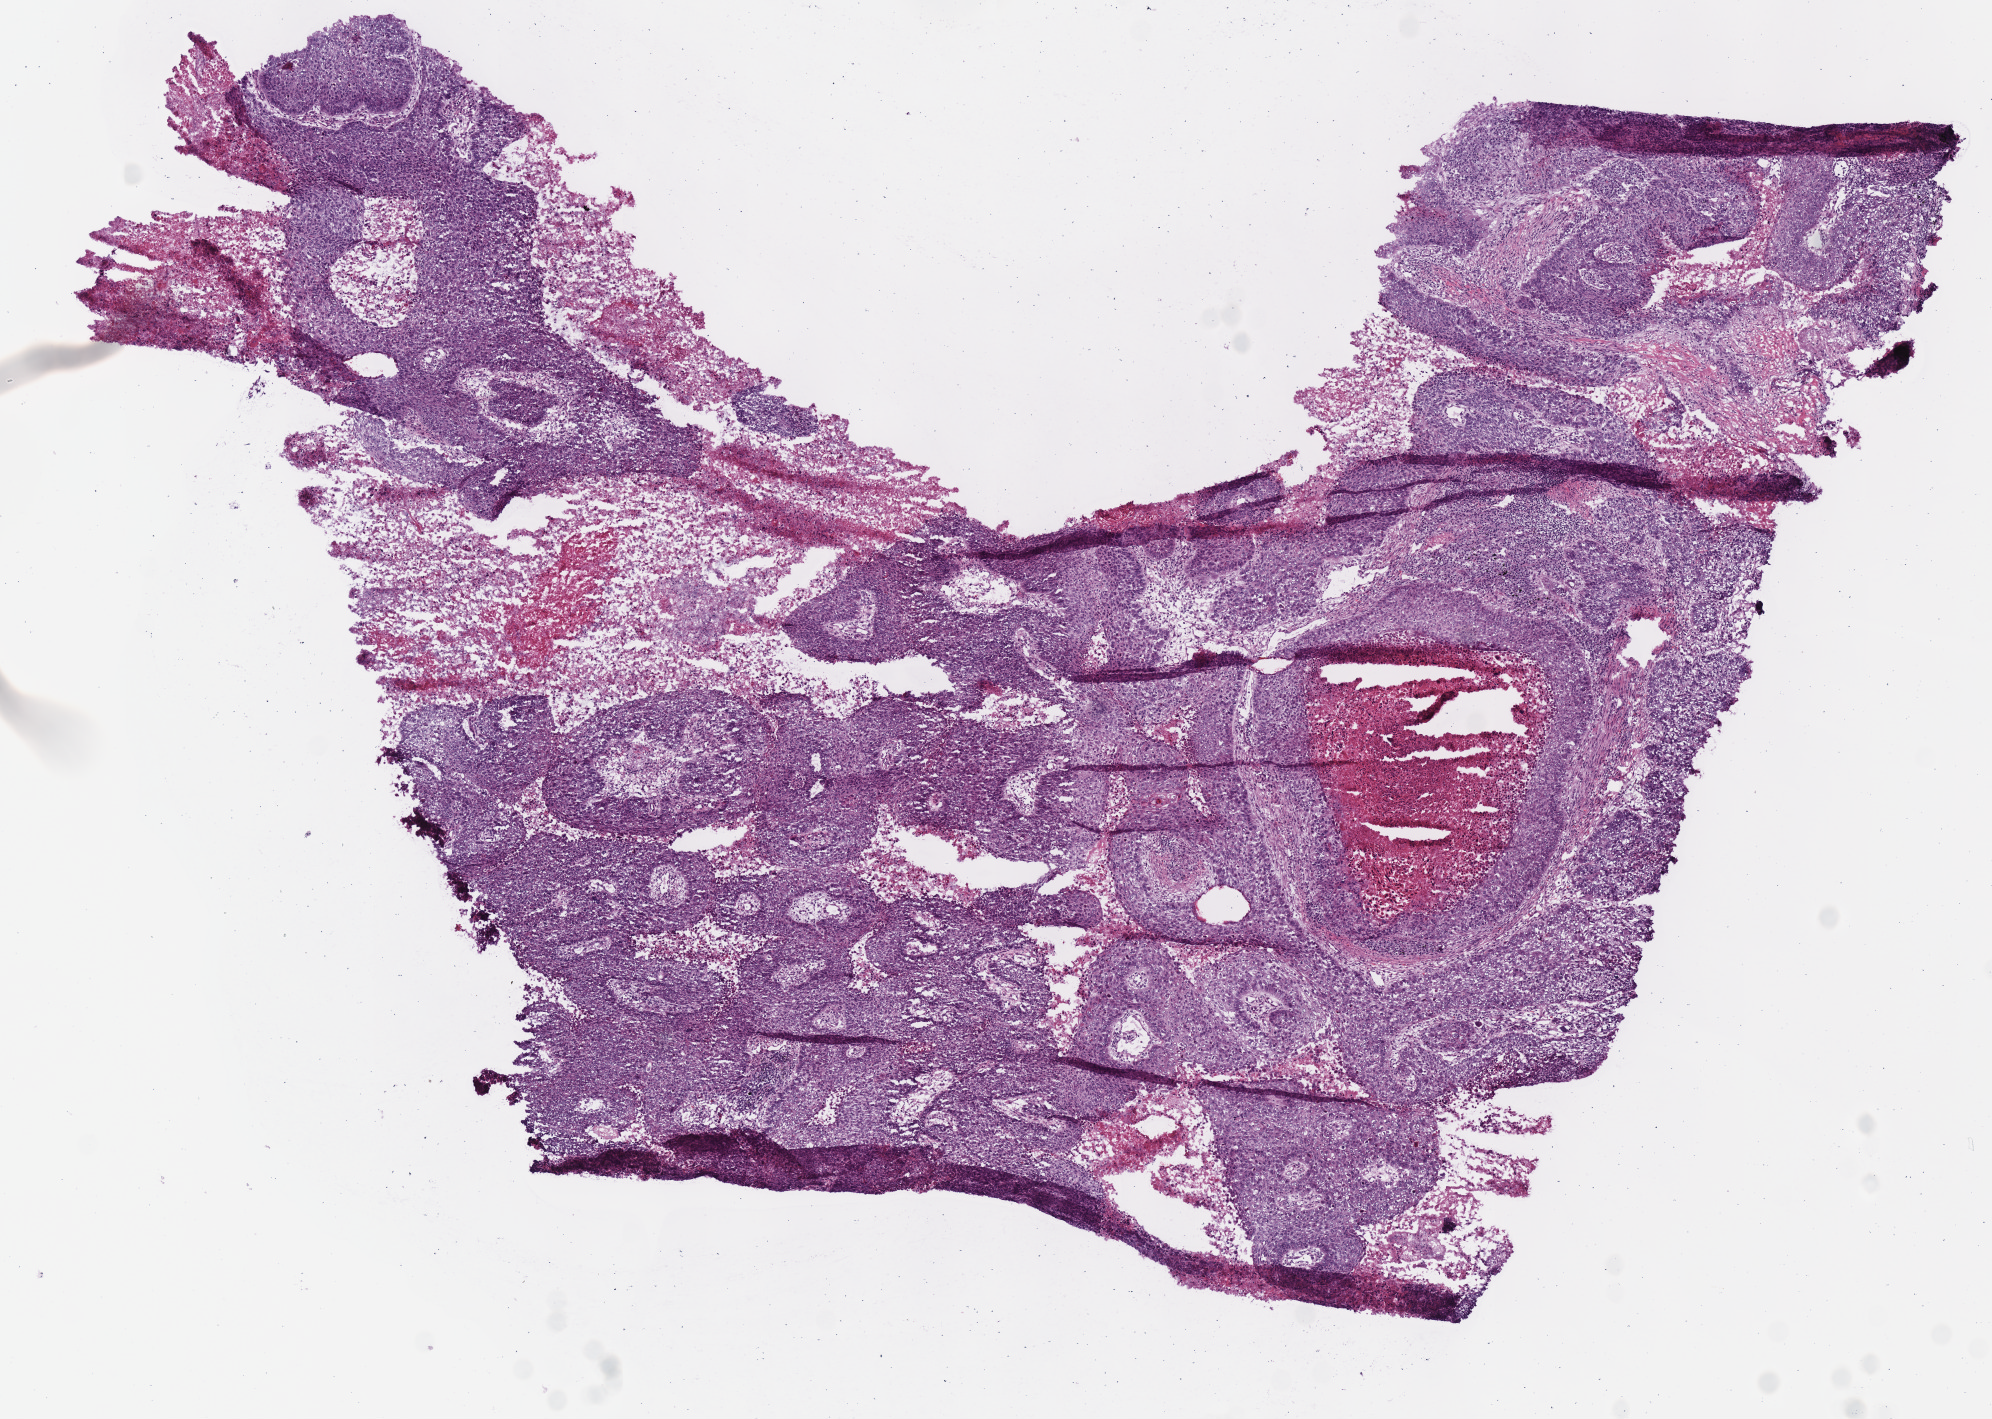
Whole-slide histology image, H&E, low-resolution overview of the scanned area, about 7.8 x 5.6 mm; frozen section from the top of the tissue portion; primary tumour sample from the lung. Patient: female, age at initial diagnosis 77 years. Pathologist review of this section (percent, as recorded): tumour cells 65%, tumour nuclei 75%, normal cells 0%, stromal cells 15%, necrosis 20%.
Pathologic diagnosis: Squamous cell carcinoma, NOS (lower lobe, lung). Laterality: right. AJCC pathologic stage: IB.